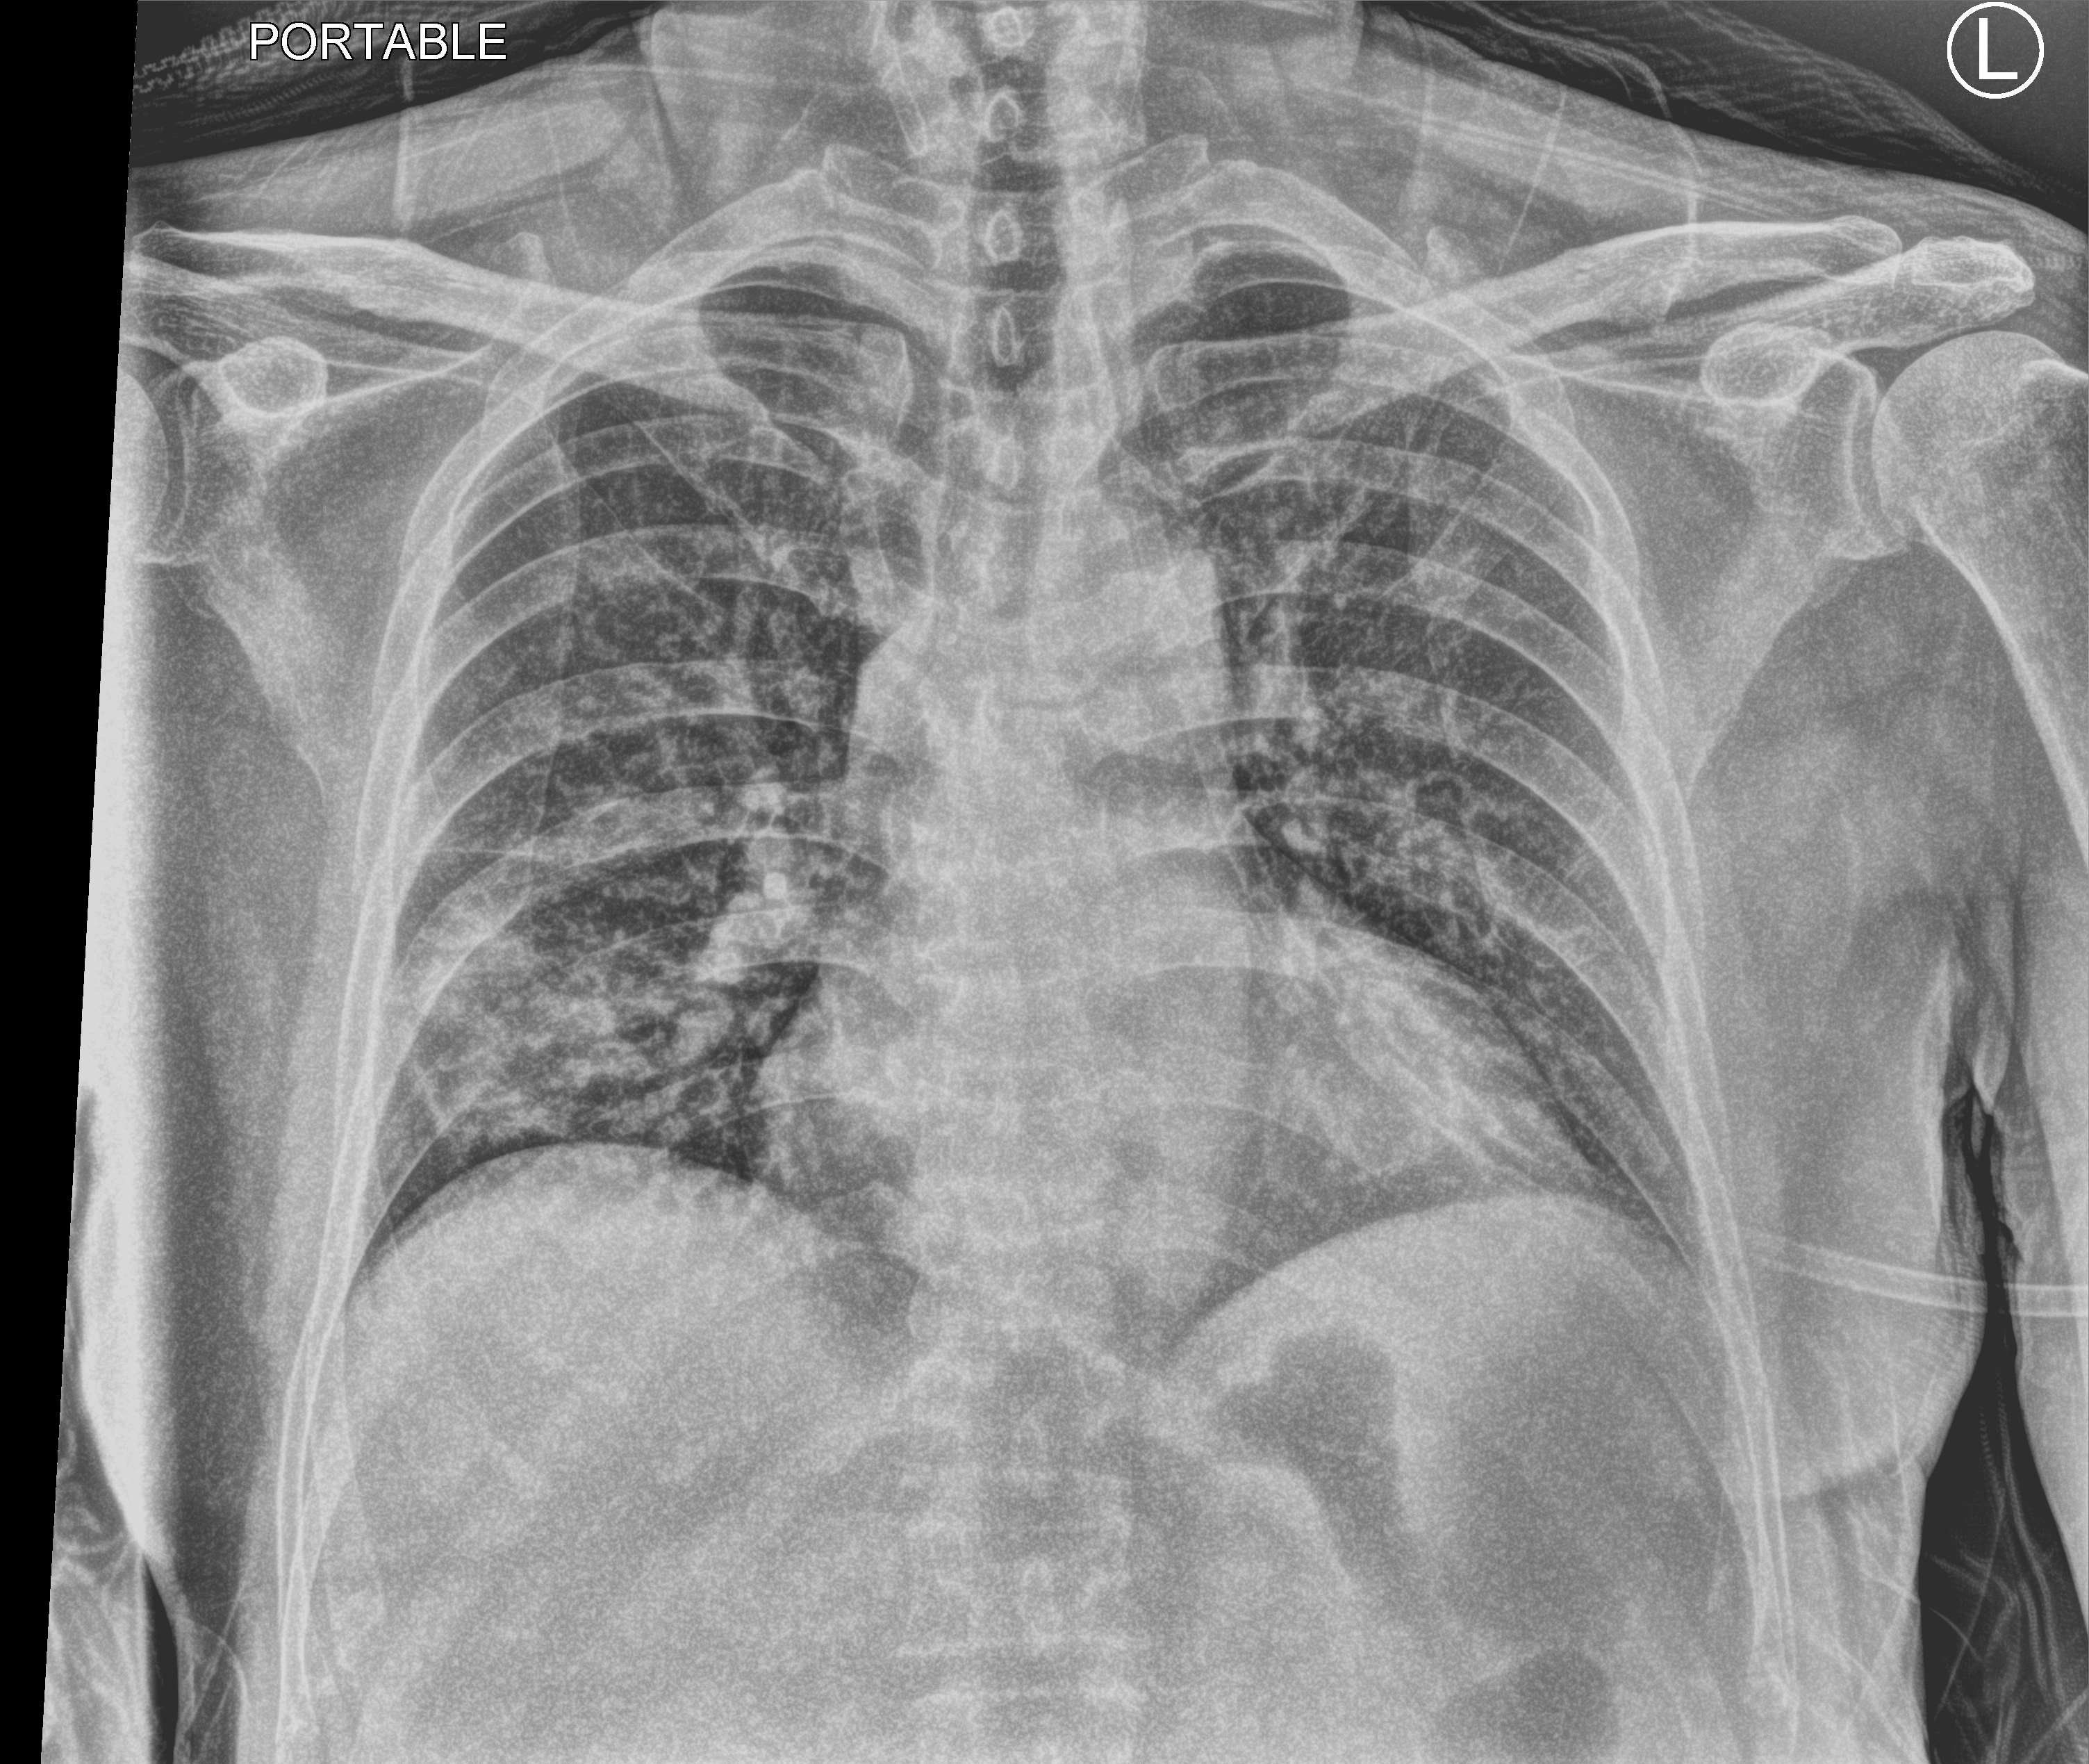
Portable chest radiograph, anteroposterior (AP) projection. Patient hospitalised with COVID-19; male, aged 60–74 years.
From the hospital-stay record, not from the radiograph (when in the stay this image was taken is not recorded):
- length of hospital stay: 20 days